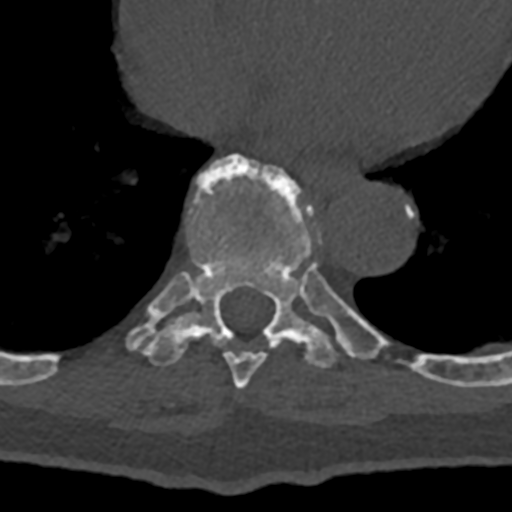
CT including the spine, one axial slice. Slice 677 of 797 in the series (ordered by position). 120 kVp. Bone window (W 1800 / L 400 HU). 0.5 mm slice thickness. 512 × 512 image matrix, field of view 160 × 160 mm. Male patient, age 74 years. From the clinical record (not read from this slice): primary cancer: renal.
Outlined on this slice (semi-automatically segmented with operator editing):
- T8 vertebra: bounding box (x1, y1, x2, y2) in pixels: (224, 285, 336, 389)
- T9 vertebra: (126, 155, 432, 379)